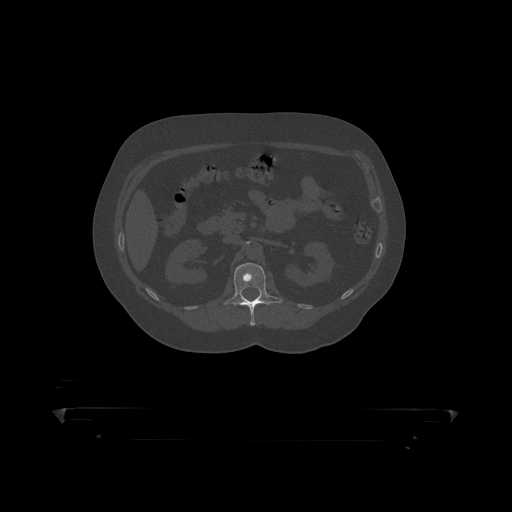
CT including the spine, one axial slice; position 146 of 390 along the scan axis; 120 kVp; bone window (W 1800 / L 400 HU); 1.25 mm slice thickness; 512 × 512 image matrix, field of view 650 × 650 mm. Patient: male, 60 years. Case-level facts recorded for this patient, not image findings: primary cancer: prostate.
Structures marked on this image (semi-automatic segmentation, software-assisted and operator-edited):
- L1 vertebra: bounding box (x1, y1, x2, y2) in pixels: (223, 263, 283, 319)